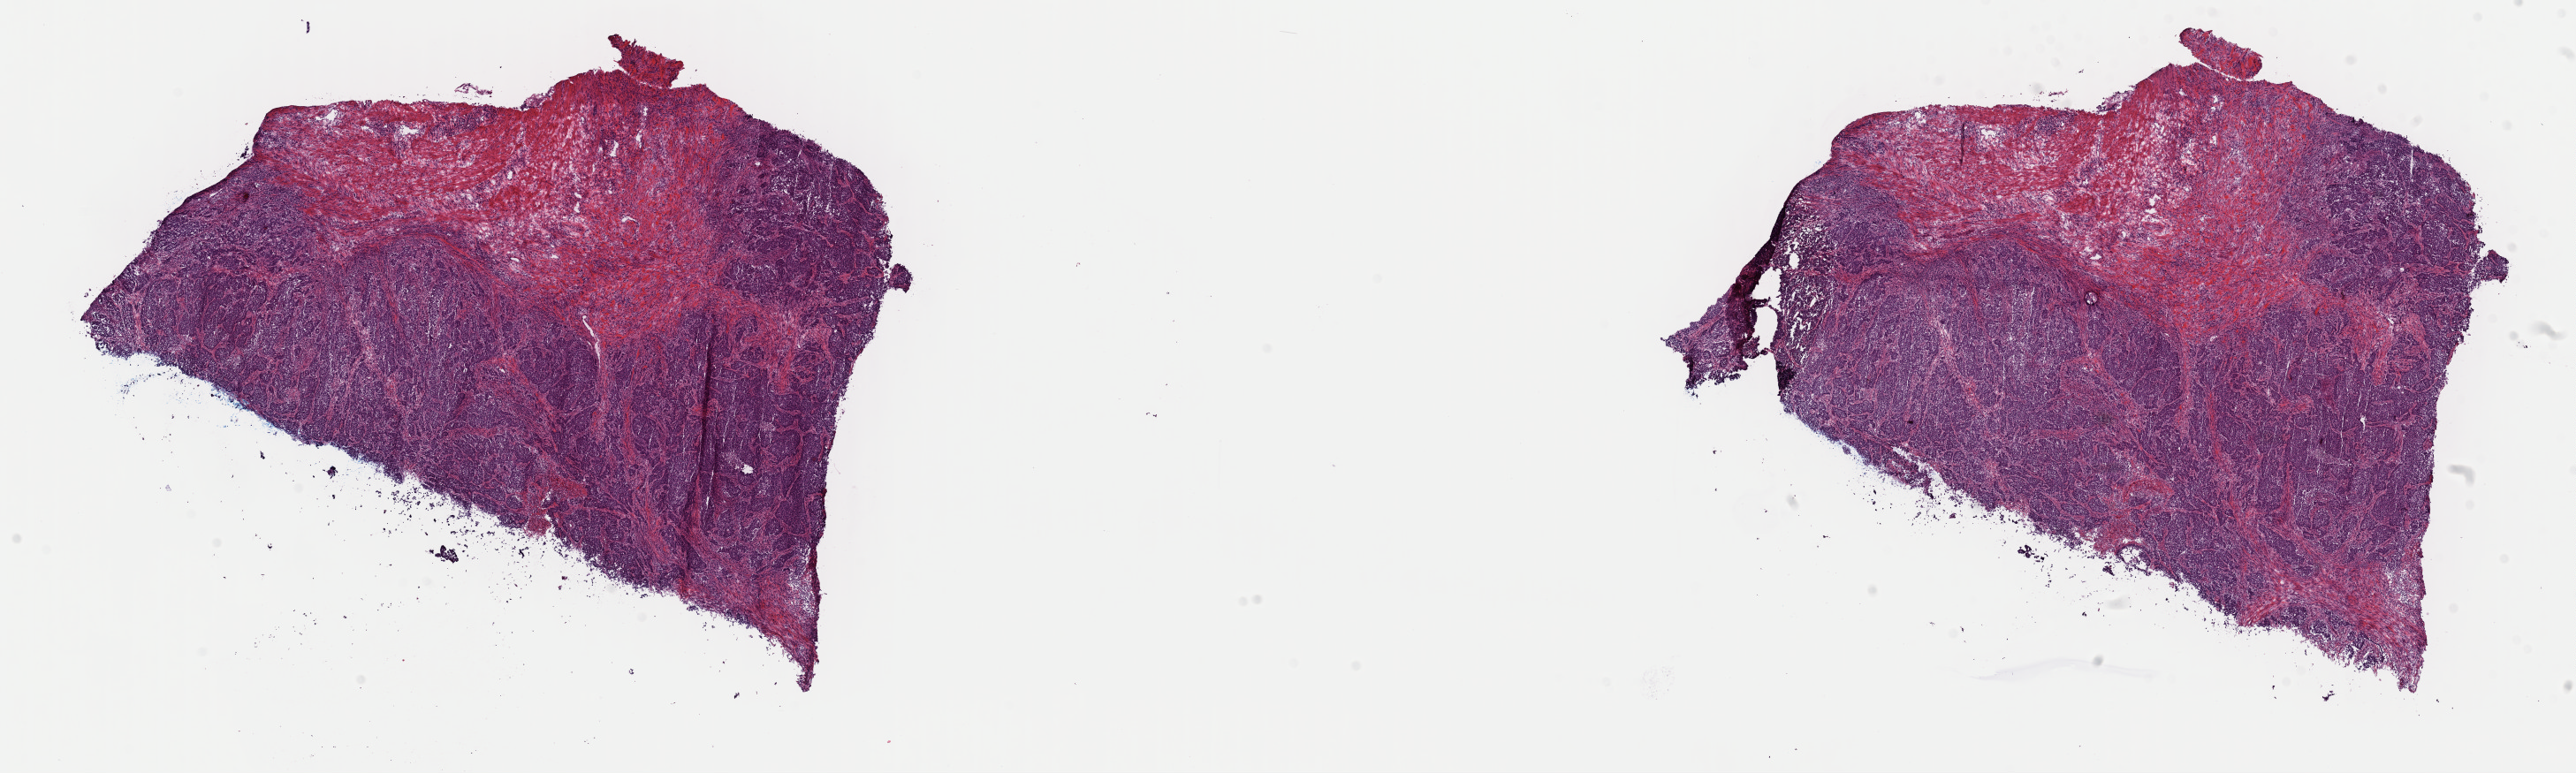
Whole-slide histology image, H&E-stained, shown as a low-resolution overview of the whole scanned area (about 23.0 x 6.9 mm, acquisition: 40x scan), frozen section, primary tumour sample from the stomach. Patient: male, age at initial diagnosis 66 years. Histologic grade: G3 (poorly differentiated). Composition of this section per pathologist review: tumour cells 60%, tumour nuclei 80%, normal cells 30%, stromal cells 10%, necrosis 0%. Inflammatory infiltration, as recorded: lymphocyte infiltration 0%, monocyte infiltration 0%, neutrophil infiltration 0%.
• AJCC pathologic stage: IIIA
• pathologic diagnosis: Adenocarcinoma, intestinal type (fundus of stomach)
• lymph nodes positive (case pathology): 3 of 17 examined
• TNM: T3 N2 M0